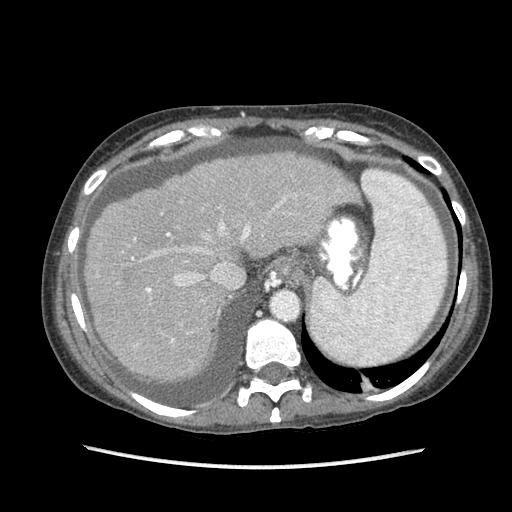
Contrast-enhanced abdominal CT (liver protocol), one axial slice; slice 70 of 87 in the series (ordered by position); soft-tissue window (W 400 / L 40 HU); 512 × 512 image matrix, field of view 340 × 340 mm. Case-level facts recorded for this patient, not image findings: diagnosis: hepatocellular carcinoma (patient treated with transarterial chemoembolisation; whether this scan precedes or follows treatment is not stated here); TNM stage (as recorded): Stage-IIIB; Child-Pugh class: A.
Annotated regions visible in this slice (semi-automatically segmented with operator editing):
- liver parenchyma outside the tumour (the mass and vessels are separate outlines, so this box may not span the whole liver): bounding box (x1, y1, x2, y2) in pixels: (84, 151, 358, 380)
- liver vessels: (131, 189, 340, 342)